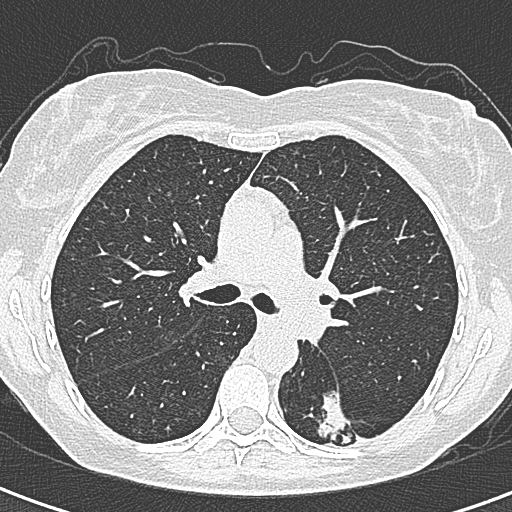
Low-dose screening chest CT, axial slice; first (baseline) screen; lung window (W 1500 / L -600 HU); 1 mm slice thickness; lung (sharp) reconstruction kernel (B80f); slice 120 of 328 in the series; 512 × 512 image matrix. Female, age 58 years at enrolment.
Lesion marked by an expert reader, bounding box [x1, y1, x2, y2] px = [291, 390, 361, 454]. The screening reader recorded 2 non-calcified nodules or masses ≥4 mm on this exam (left lower lobe, right lower lobe); which of them this box marks is not recorded. Official screen result: positive, change unspecified: nodule(s) >= 4 mm or enlarging nodule(s), mass(es), or other non-specific abnormalities suspicious for lung cancer. Lung cancer was diagnosed 22 days after this screen: adenocarcinoma, NOS, left lower lobe, moderately differentiated (G2), stage IA (AJCC 6th edition), 25 mm at pathology.